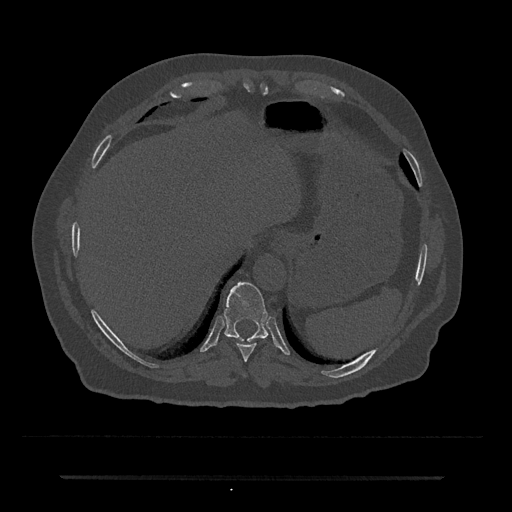
CT including the spine, one axial slice. Slice 249 of 797 in the series (ordered by position). Bone window (W 1800 / L 400 HU). 0.5 mm slice thickness. 512 × 512 image matrix, field of view 437 × 437 mm. Male patient, age 69 years. Case-level facts recorded for this patient, not image findings: primary cancer: prostate.
Annotated regions visible in this slice (semi-automatically segmented with operator editing):
- T10 vertebra: bounding box (x1, y1, x2, y2) in pixels: (224, 282, 268, 342)
- T9 vertebra: (236, 343, 257, 362)